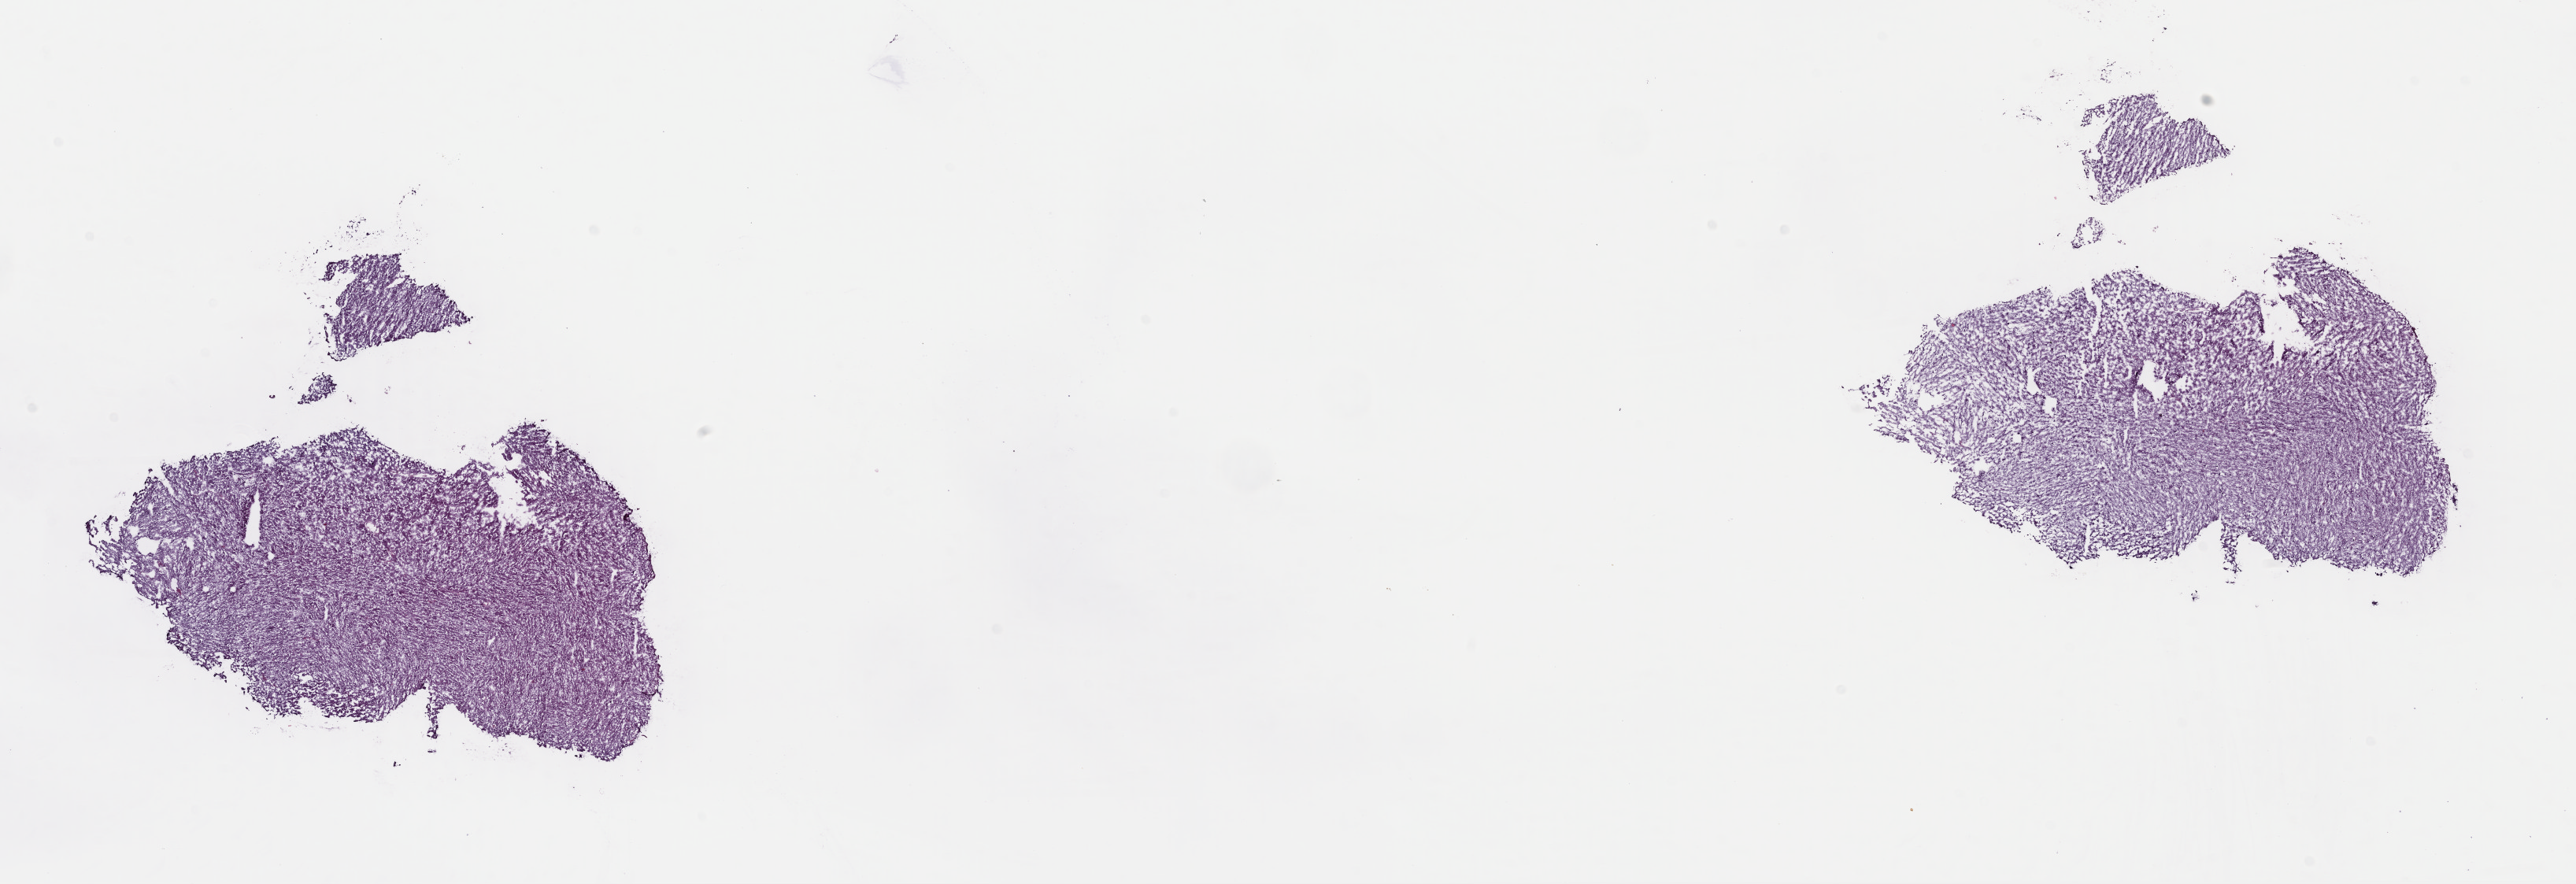
Whole-slide histology image, Hematoxylin and eosin (H&E) stained, shown as a low-resolution overview of the whole scanned area (about 25.7 x 8.8 mm, slide scanned at 40x); frozen section from the top of the tissue portion; primary tumour sample from the brain. Male patient; age at initial diagnosis 33 years. Histologic grade: G2 (moderately differentiated). Composition of this section per pathologist review: tumour cells 40%, tumour nuclei 80%, normal cells 10%, stromal cells 50%, necrosis 0%. Inflammatory infiltration, as recorded: lymphocyte infiltration 0%, monocyte infiltration 0%, neutrophil infiltration 0%.
Laterality: right. Pathologic diagnosis: Oligodendroglioma, NOS.